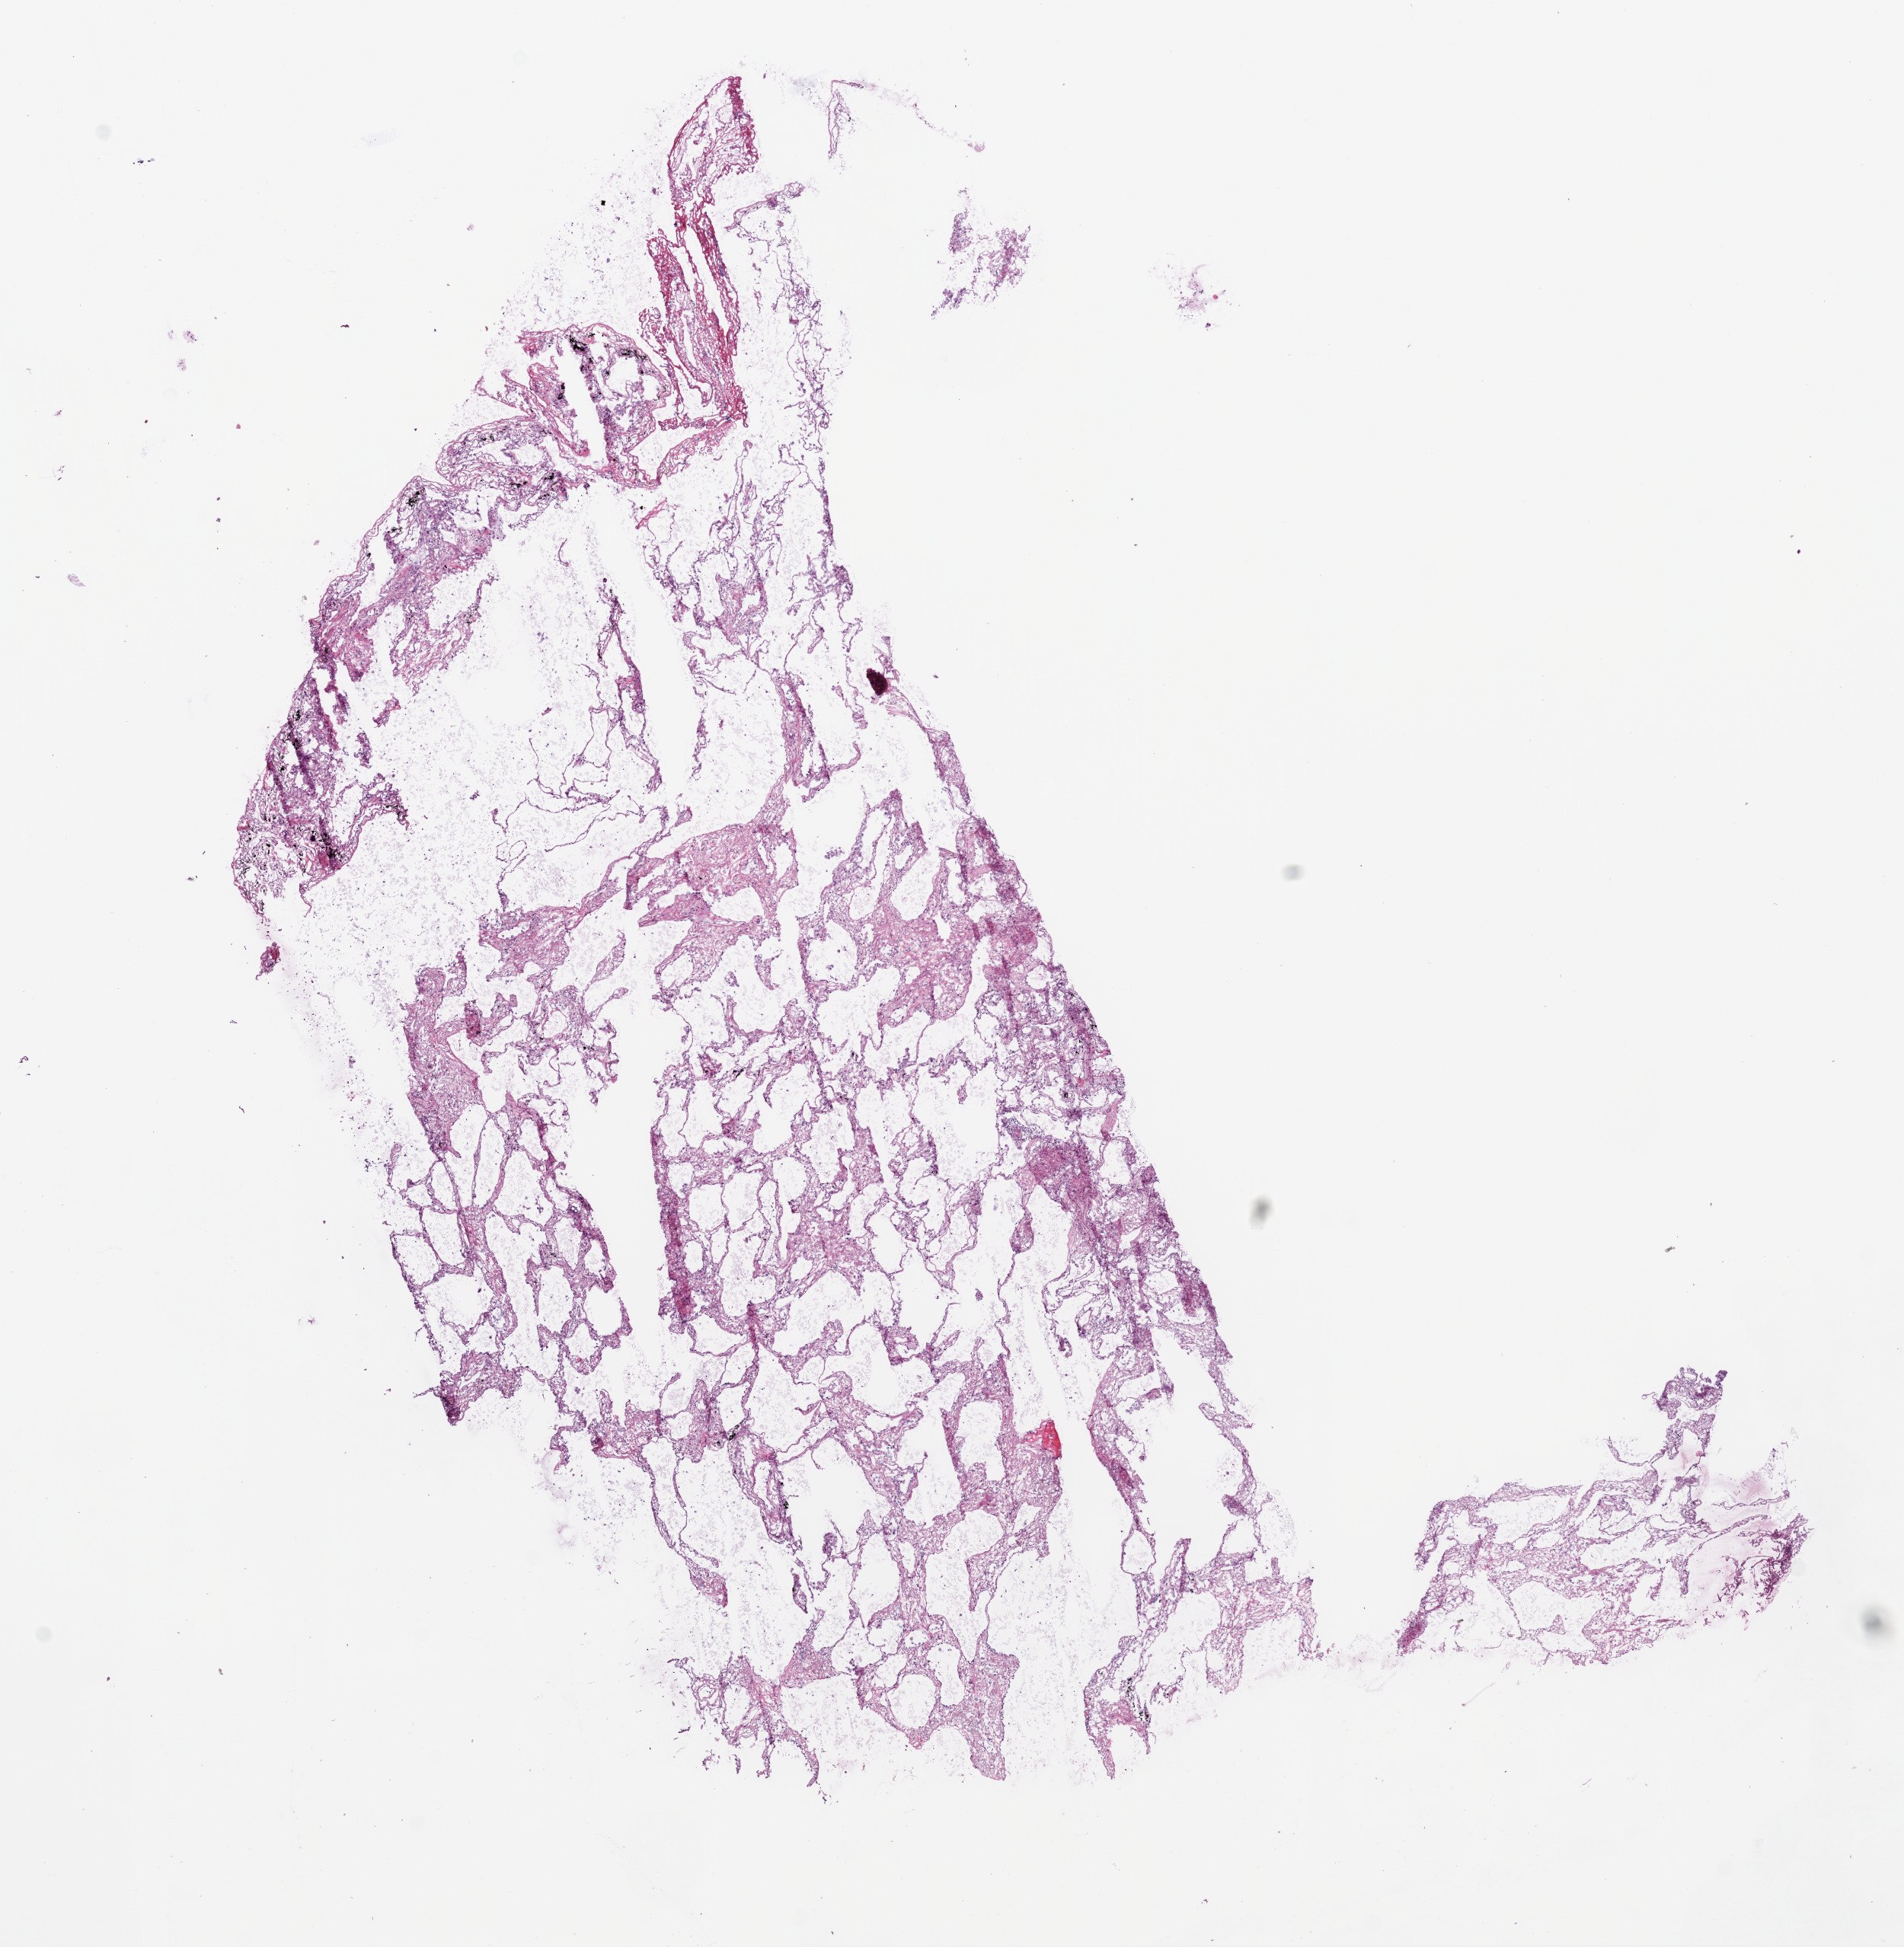
Hematoxylin and eosin (H&E) stained whole-slide image, low-resolution overview of the scanned area, about 10.0 x 10.3 mm; frozen section from the bottom of the tissue portion; lung, solid tissue normal (non-tumour tissue) sample. Female patient; age at initial diagnosis 76 years.
This section: solid tissue normal (non-tumour) sample from the same patient. Patient diagnosis: Squamous cell carcinoma, NOS (upper lobe, lung).